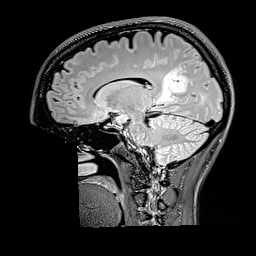
Brain MRI from a brain-tumour surgery series, one sagittal slice. Slice 99 of 176 in the series (ordered by position). T2 FLAIR. 256 × 256 image matrix, field of view 256 × 256 mm. Case-level facts recorded for this patient, not image findings: histopathology: Oligodendroglioma; WHO grade: 2; IDH mutation: yes; tumour location: Right Parietal.
Annotated regions visible in this slice (expert manual segmentation):
- tumour: box from (x=159, y=65) to (x=188, y=103) px